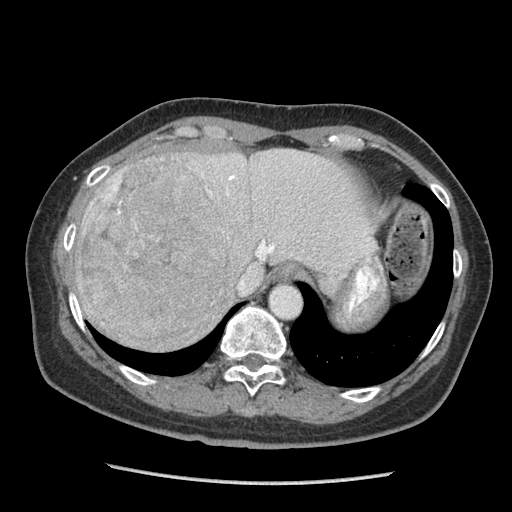
Contrast-enhanced abdominal CT (liver protocol), one axial slice. Slice 73 of 105 in the series (ordered by position). Reconstruction kernel STANDARD. 140 kVp. Soft-tissue window (W 400 / L 40 HU). 512 × 512 image matrix, field of view 340 × 340 mm. From the clinical record (not read from this slice): diagnosis: hepatocellular carcinoma (patient treated with transarterial chemoembolisation; whether this scan precedes or follows treatment is not stated here); TNM stage (as recorded): Stage-I; Child-Pugh class: A; tumour differentiation: moderately differentiated; tumour nodularity: uninodular.
Annotated regions visible in this slice (semi-automatically segmented with operator editing):
- abdominal aorta: bounding box (x1, y1, x2, y2) in pixels: (271, 286, 300, 317)
- liver parenchyma outside the tumour (the mass and vessels are separate outlines, so this box may not span the whole liver): (68, 148, 373, 348)
- mass: (75, 155, 229, 349)
- liver vessels: (227, 175, 275, 252)